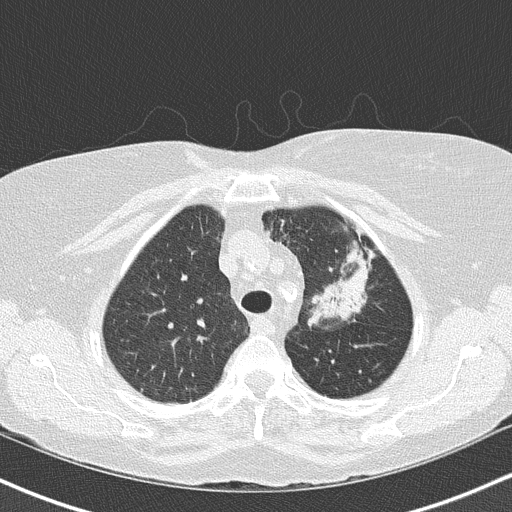
Axial slice from a low-dose chest CT screening exam. Third annual screen. Lung window (W 1500 / L -600 HU). 2 mm slice thickness. 120 kVp. Slice 118 of 147 in the series. 512 × 512 image matrix. Female, age 68 years at enrolment. Former smoker at enrolment.
• Expert-annotated lung lesion, bounding box [x1, y1, x2, y2] px = [295, 223, 381, 330].
• Reader record for this screening exam (exam-level; its link to the box is not recorded): non-calcified nodule or mass ≥4 mm, left upper lobe, 5 × 5 mm, poorly defined margins, mixed attenuation, pre-existing on the prior screen: yes; interval growth: yes.
• Official screen result: positive, other.
• Lung cancer was diagnosed 42 days after this screen: adenocarcinoma, NOS, left upper lobe, poorly differentiated (G3), stage IB (AJCC 6th edition), 50 mm at pathology.